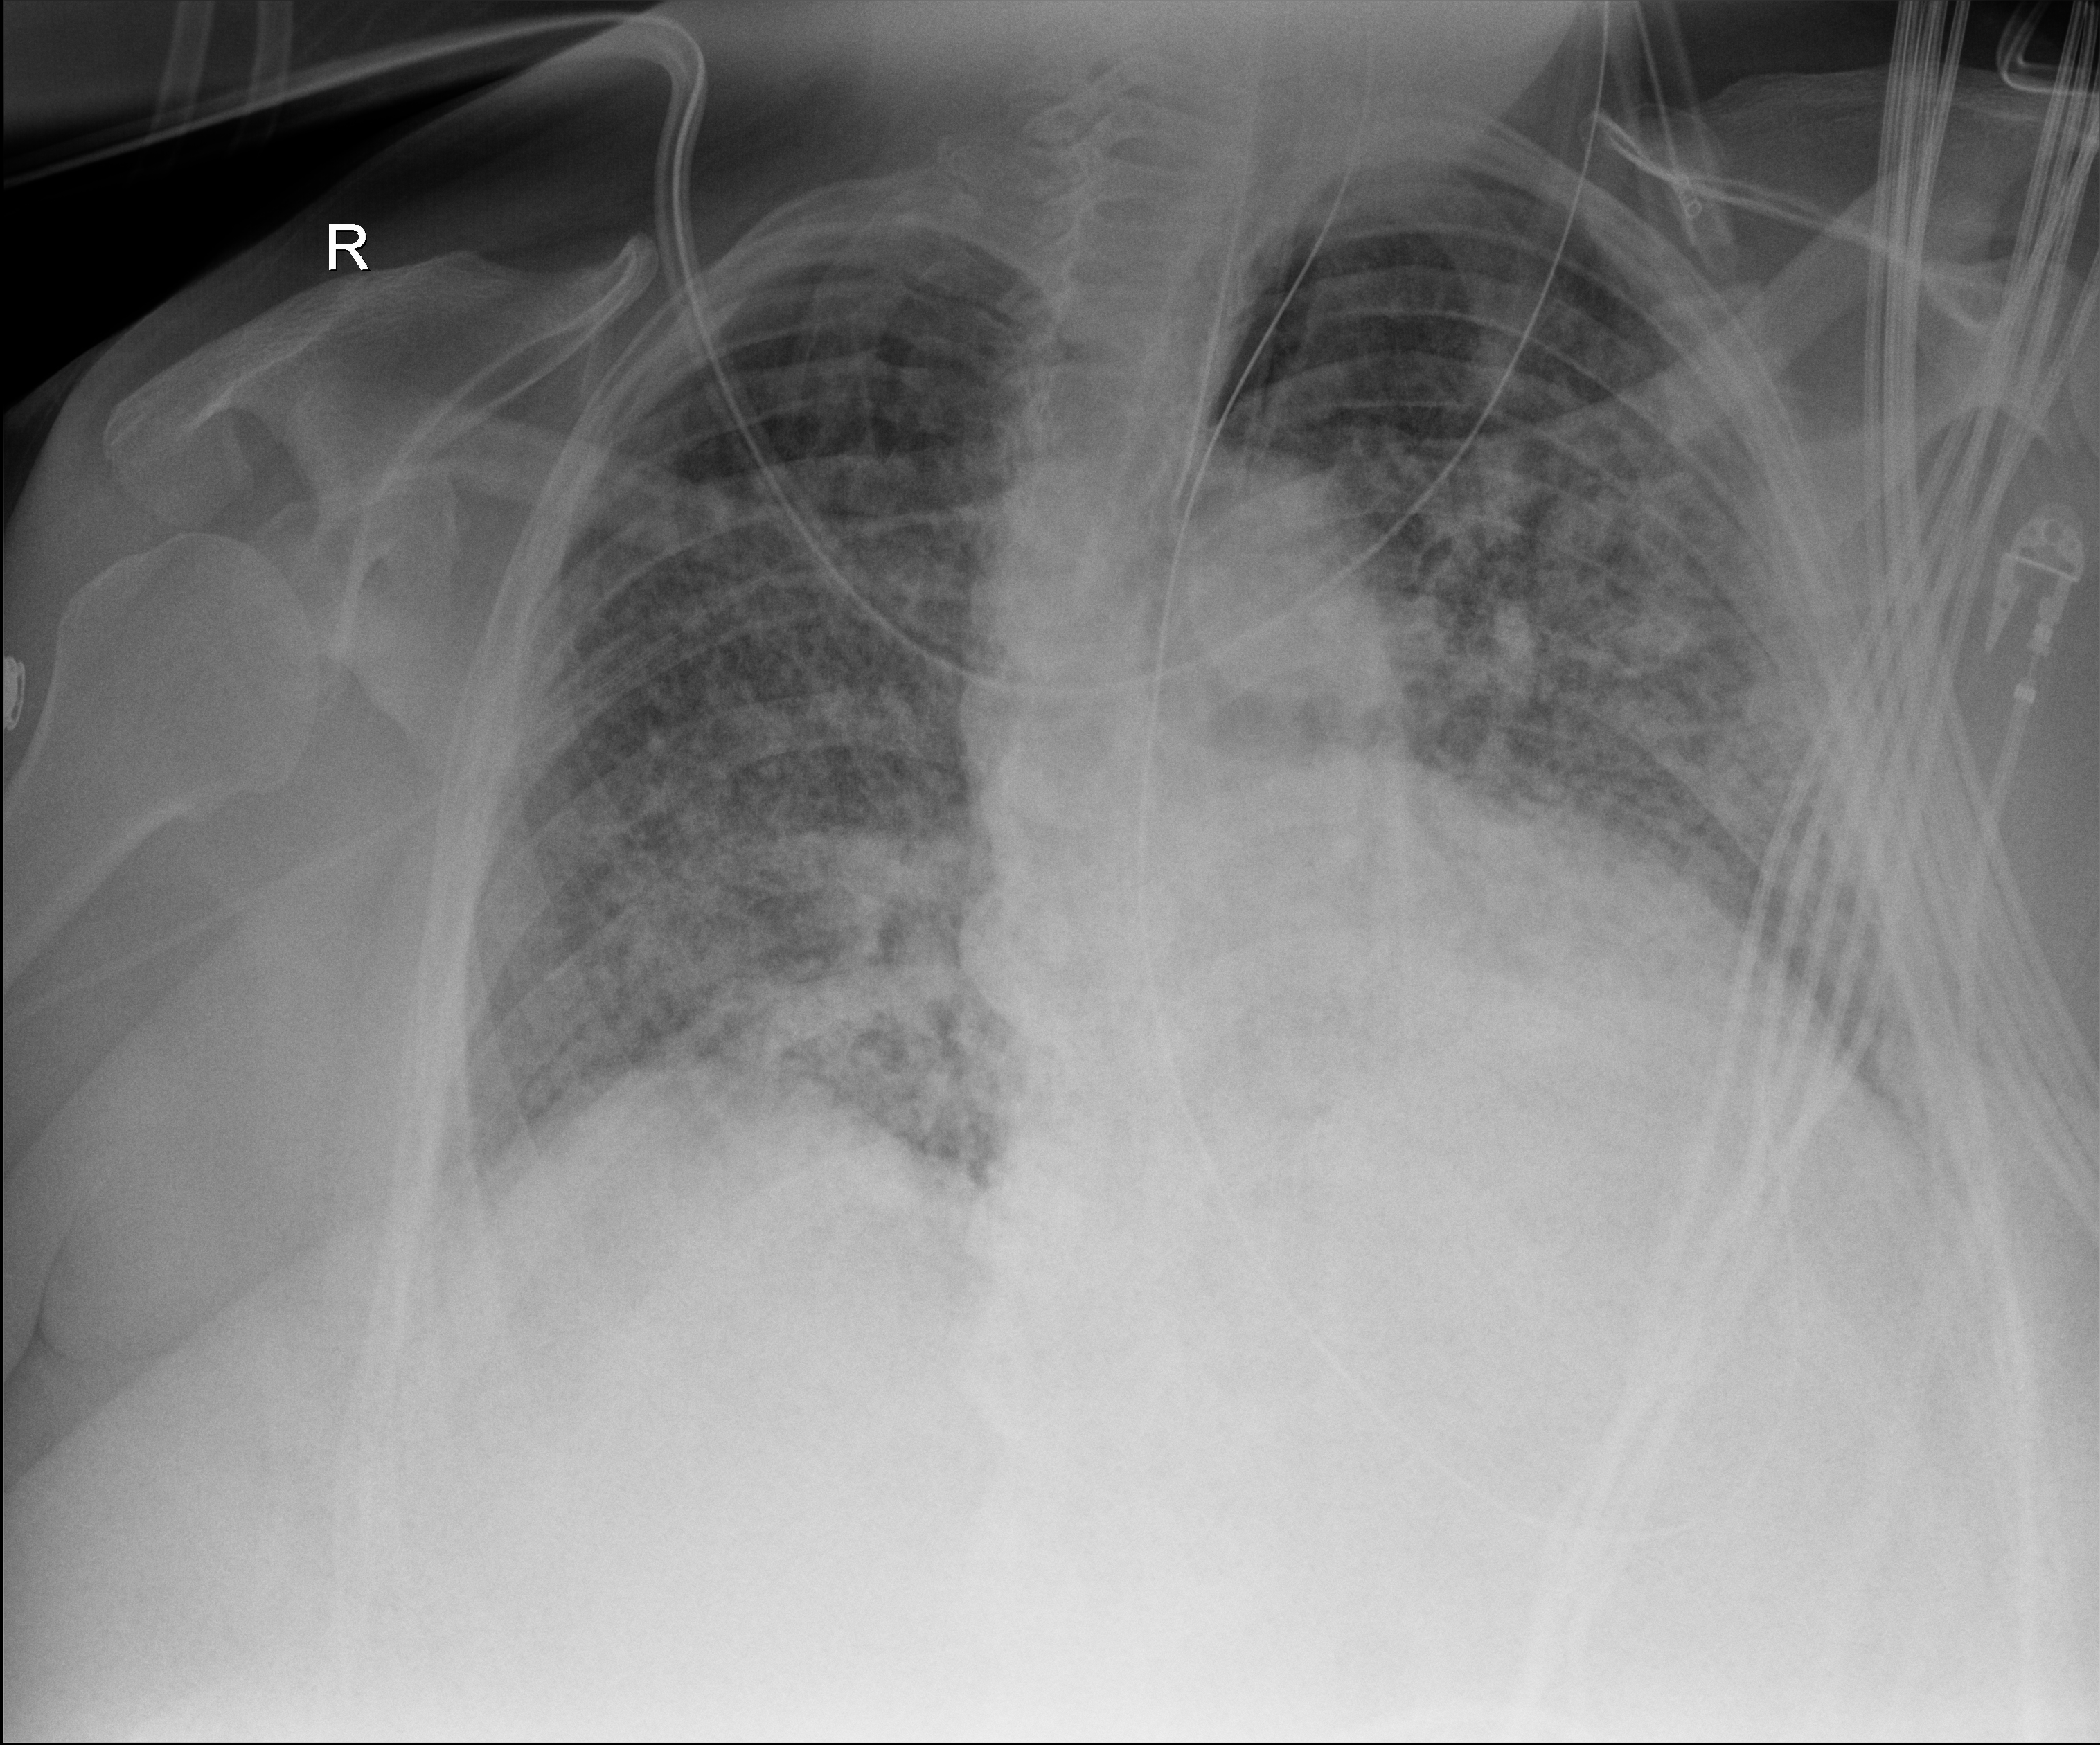
Chest radiograph (digital radiography); anteroposterior (AP) projection. Patient hospitalised with COVID-19, aged 18–59 years.
Hospital-stay facts (about this admission, not read from this image; timing relative to this image not recorded): mechanically ventilated during this hospital stay: yes.